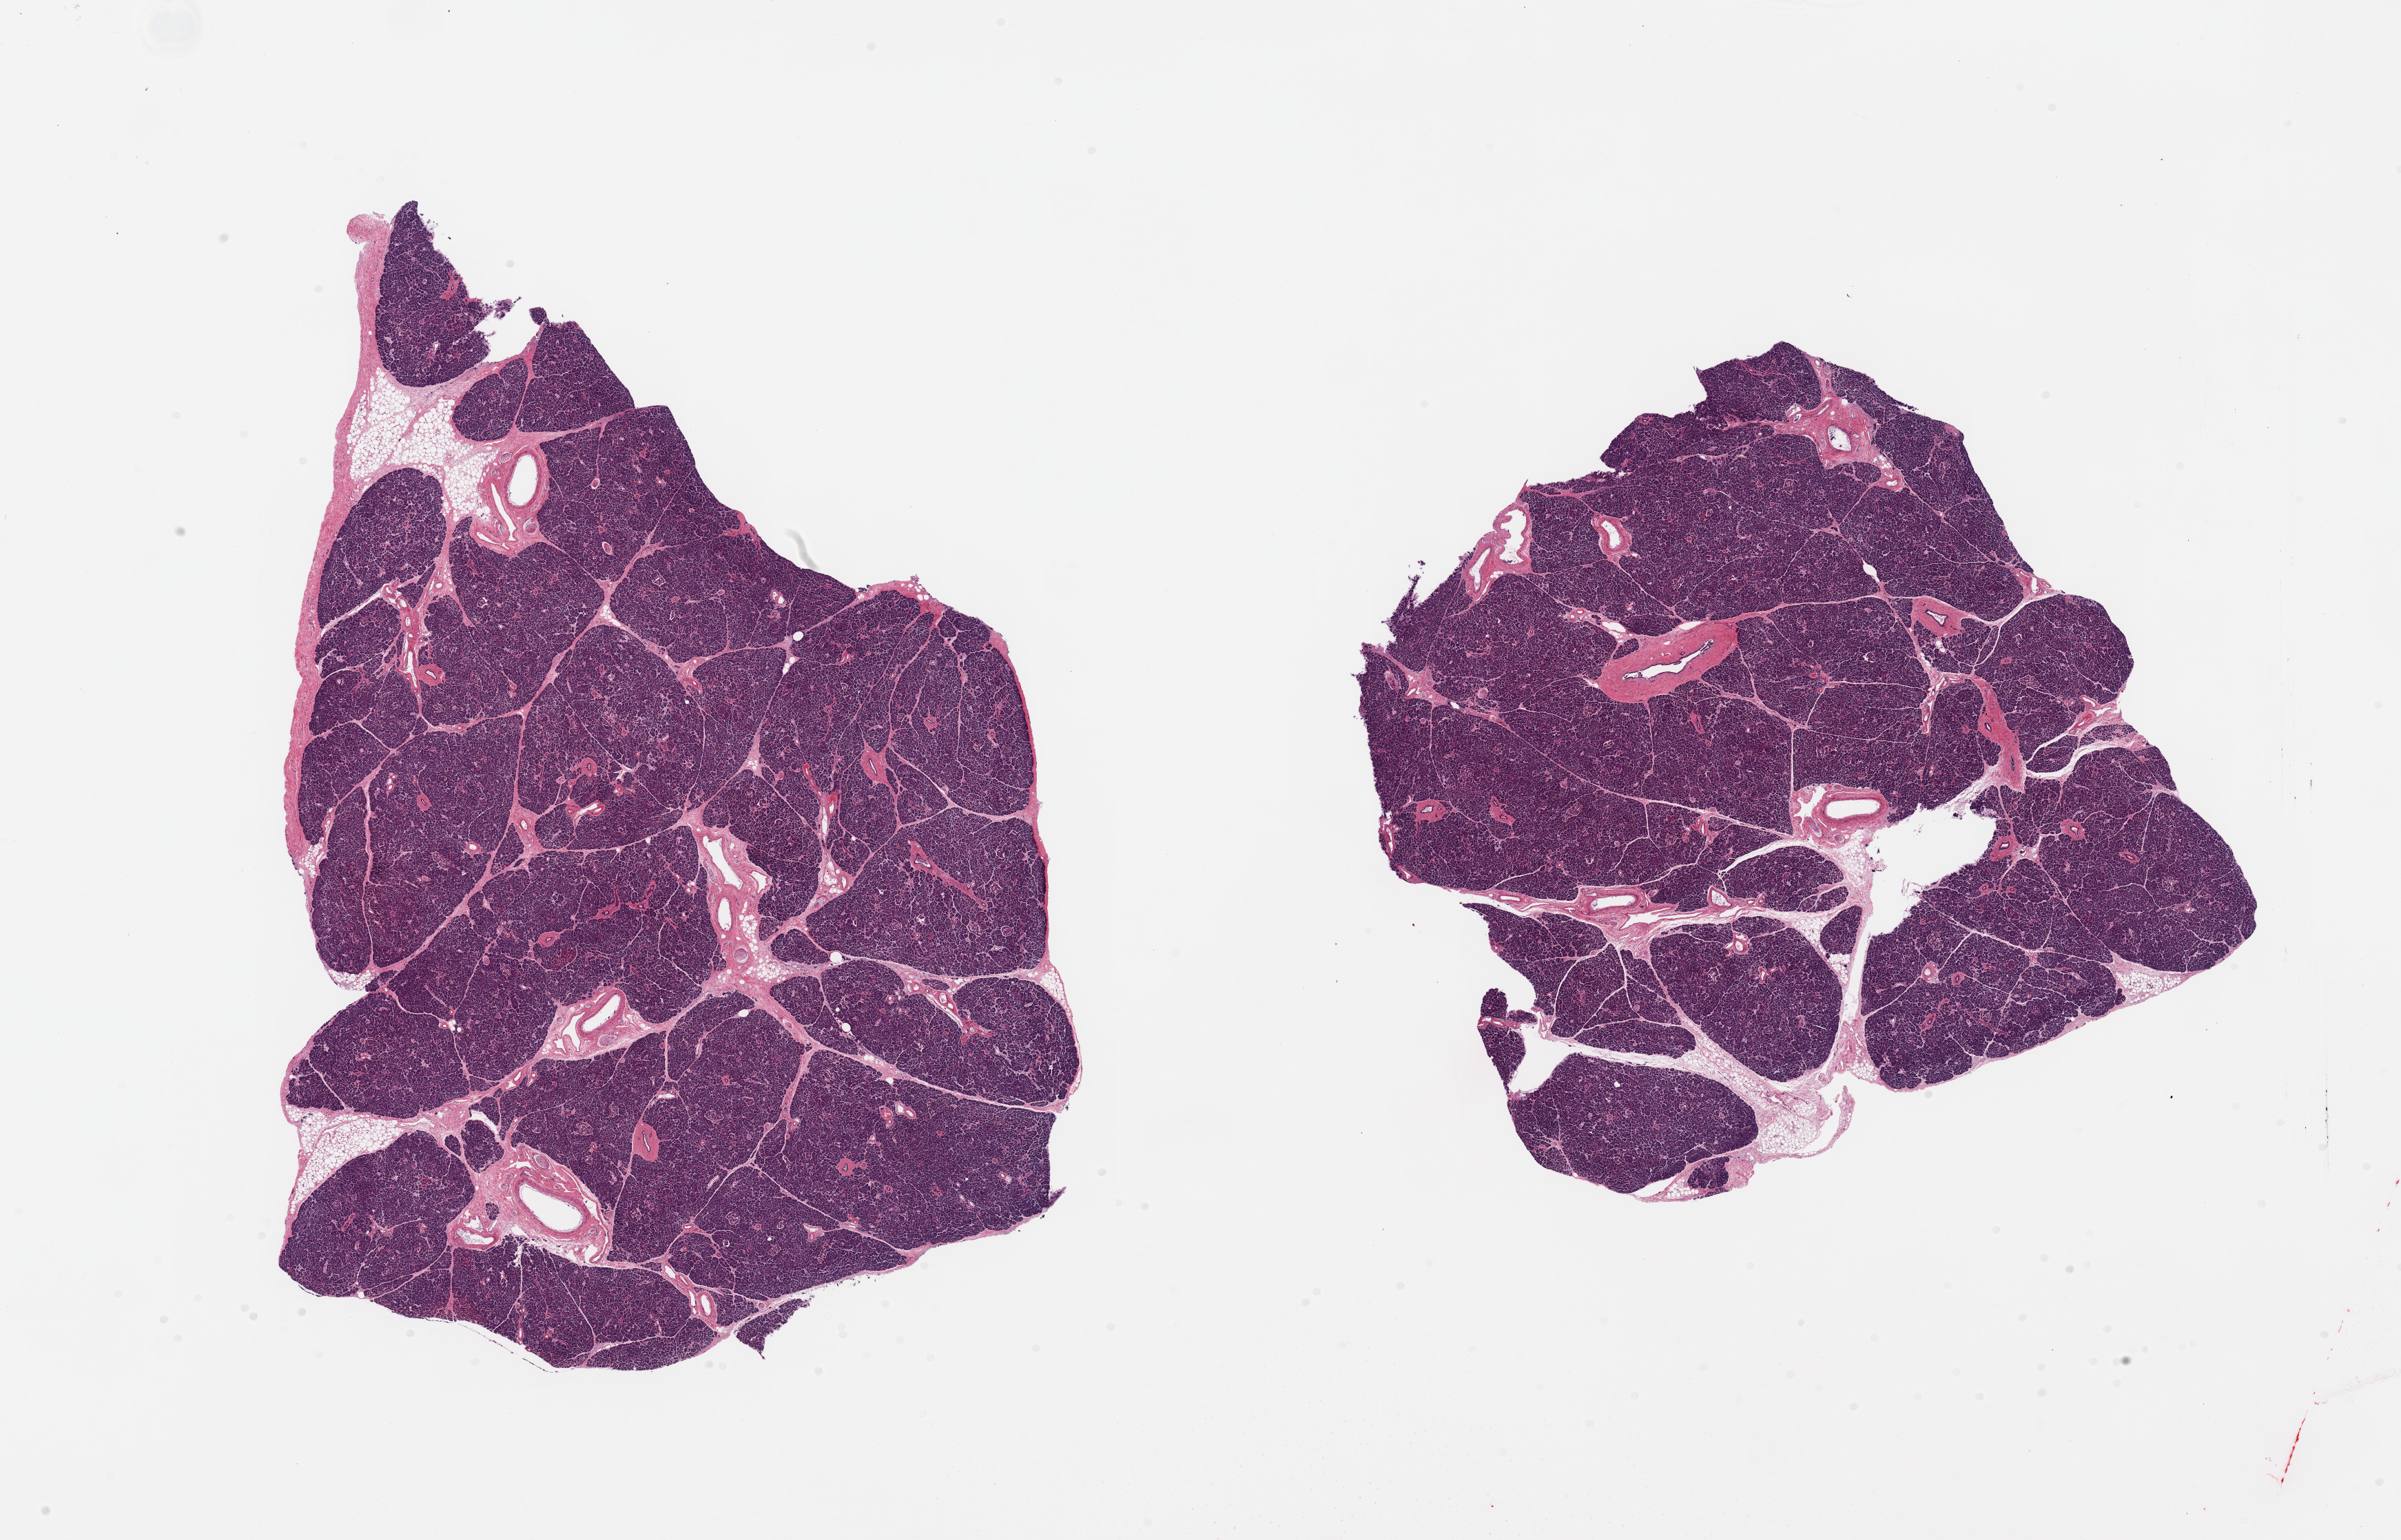
Haematoxylin and eosin whole-slide image, low-resolution overview of the scanned area, about 27.6 x 17.7 mm; PAXgene-fixed, paraffin-embedded tissue; sampled site (target tissue): pancreas; tissue donor sample. Donor: female.
* review note (as recorded): 2 pieces; insignificant internal fat; well preserved parenchyma, representative islets marked